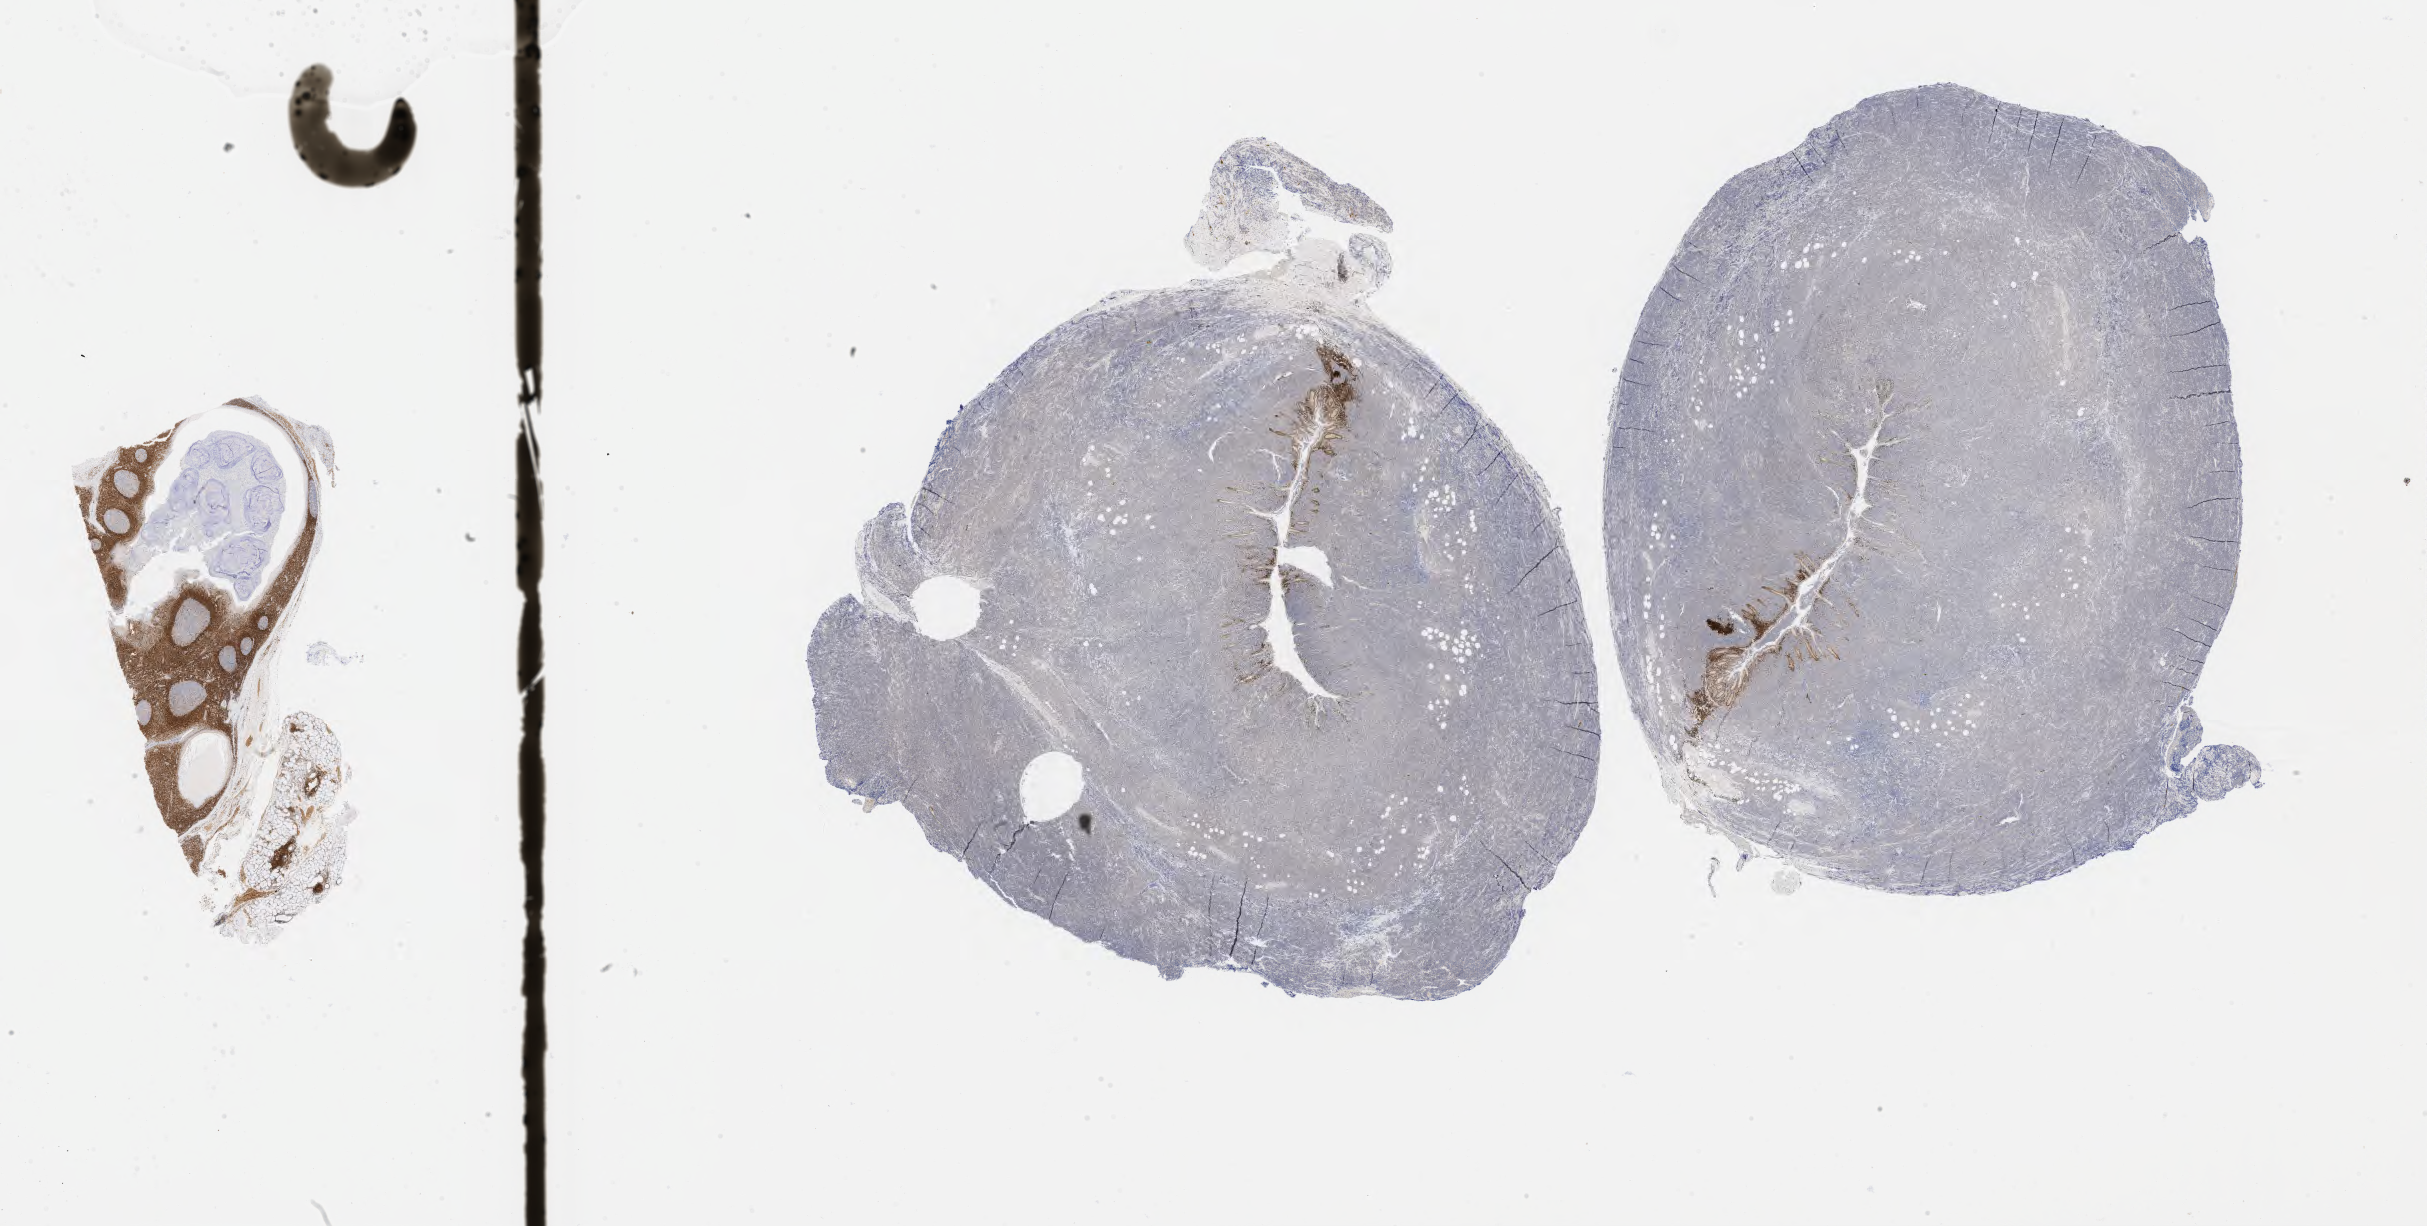
IHC for BCL2, whole-slide image, a low-resolution overview of the entire scanned area, about 39.3 x 19.8 mm, specimen: tumor tissue. Male patient, aged 63.
Diagnosis: Diffuse large B-cell lymphoma, NOS.